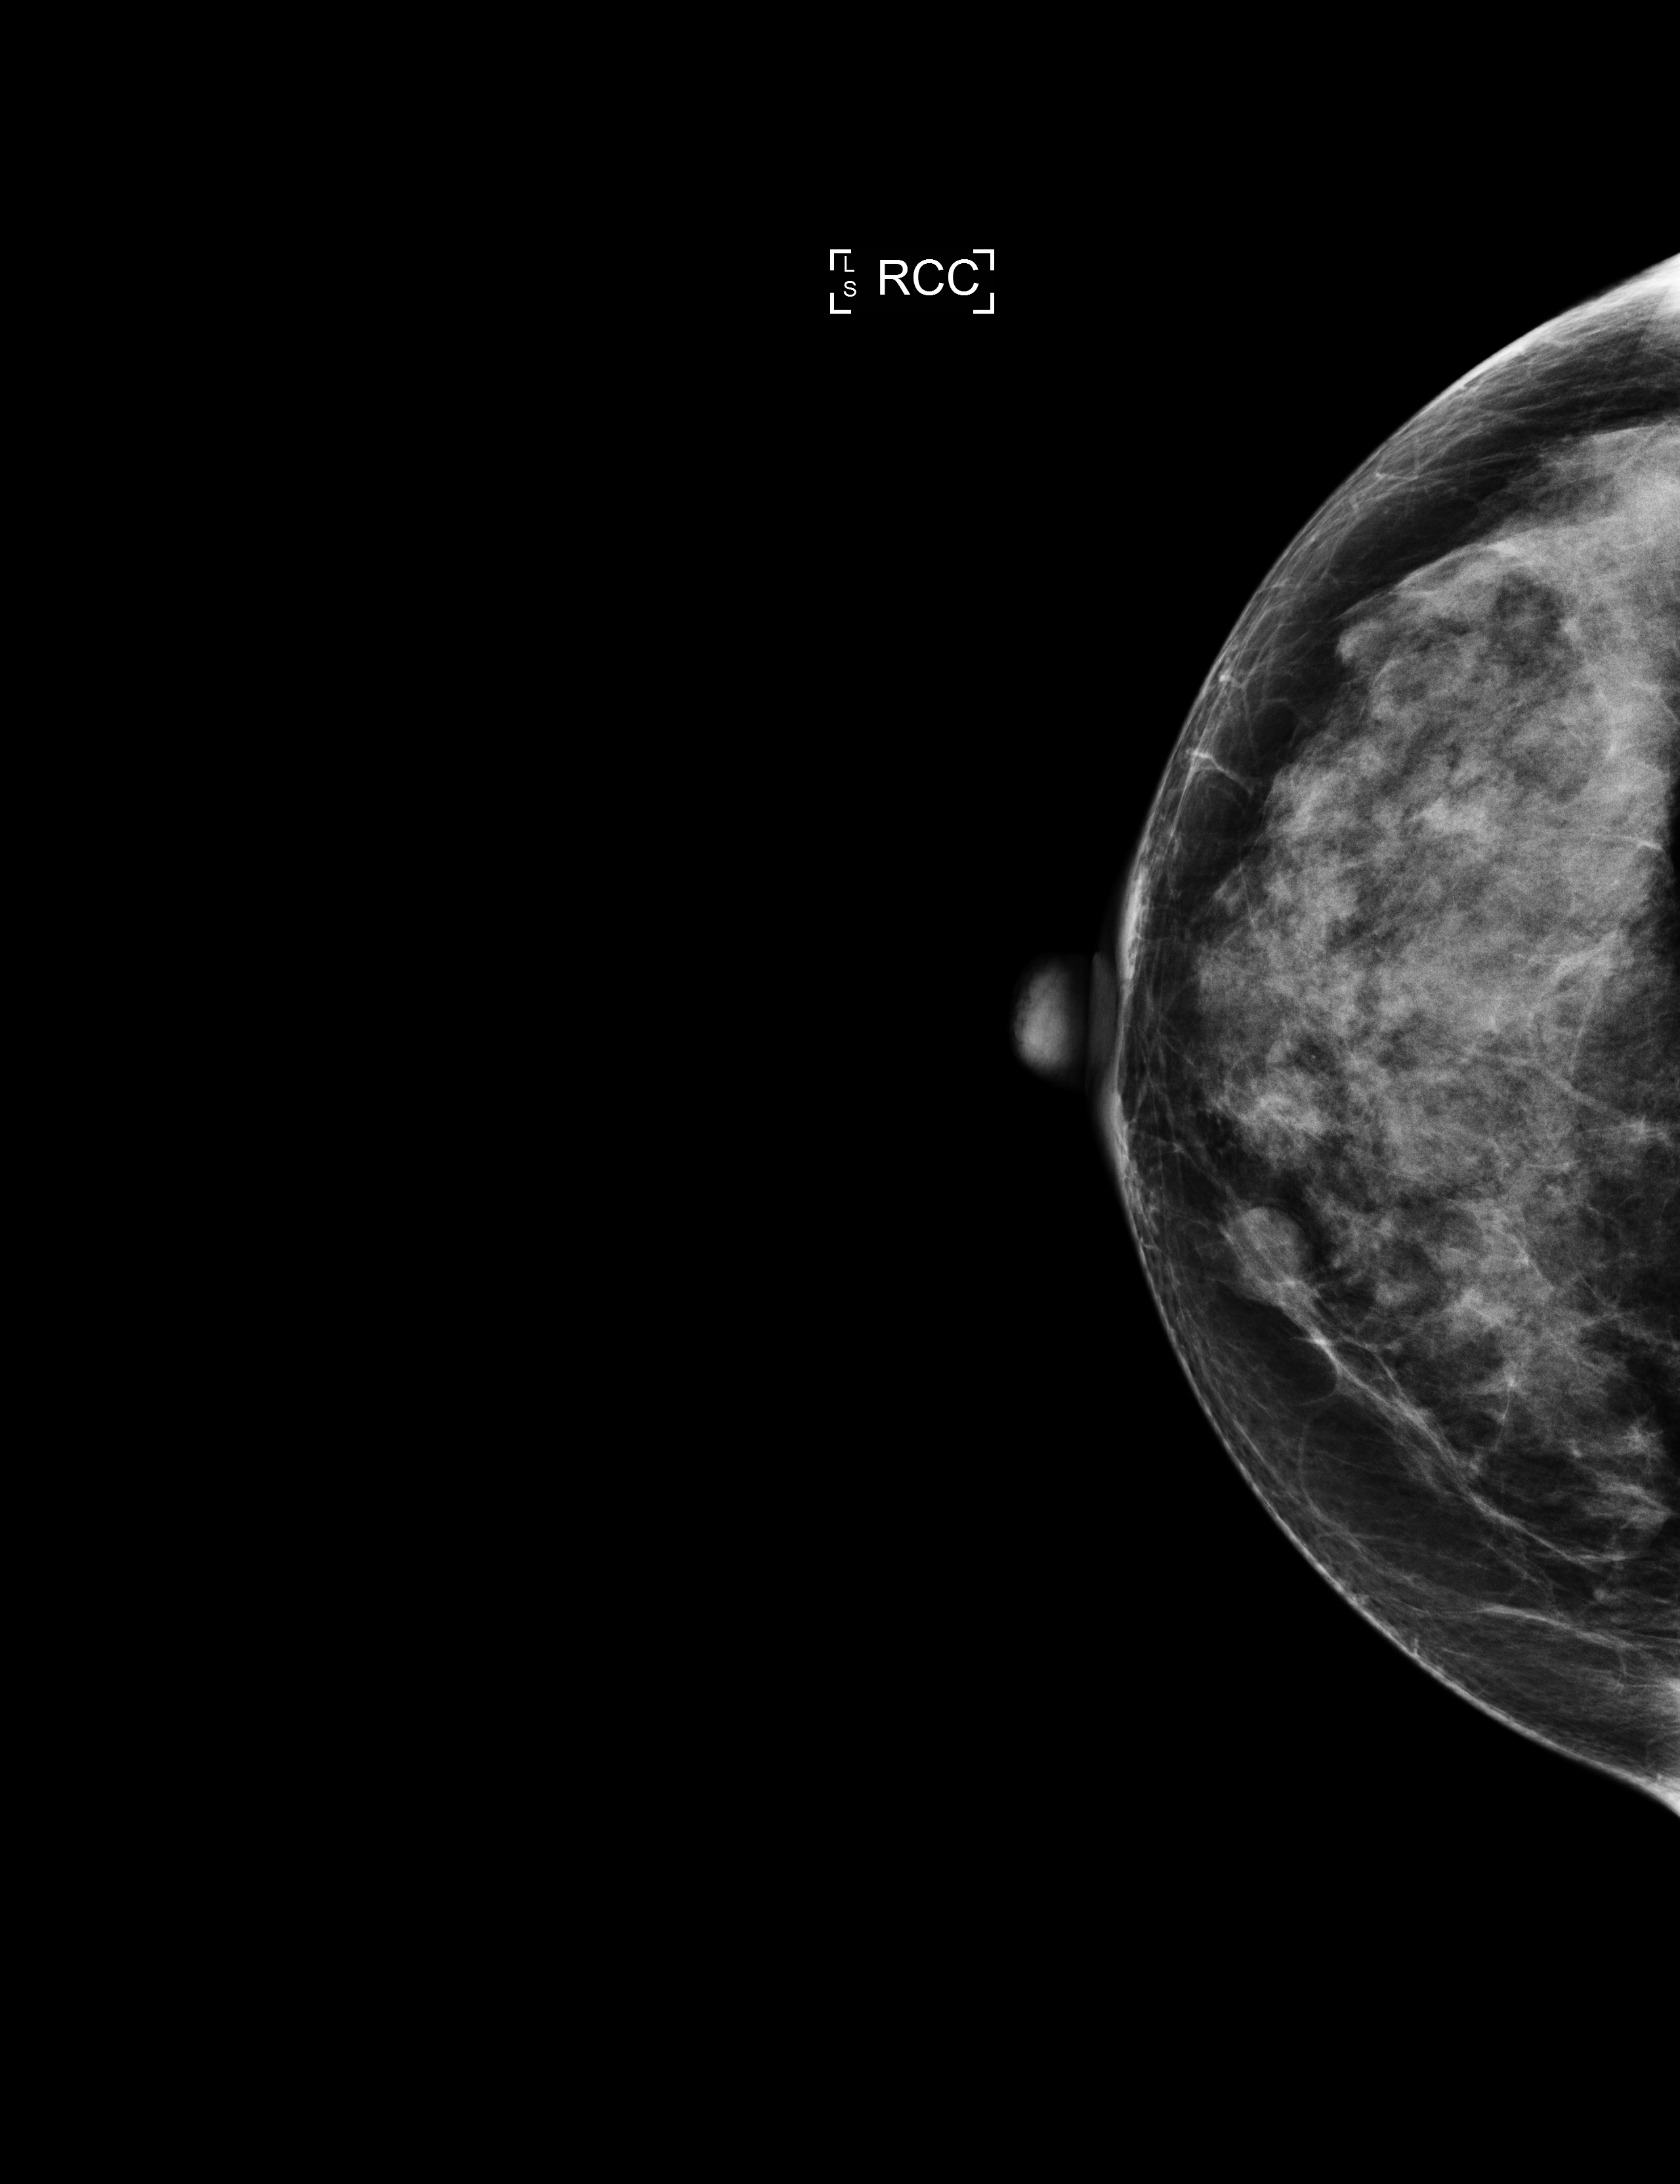
Annual screening mammography examination. Patient: female, 67 years.
Image type: full-field digital mammogram. Breast: right. Projection: craniocaudal (CC) view.